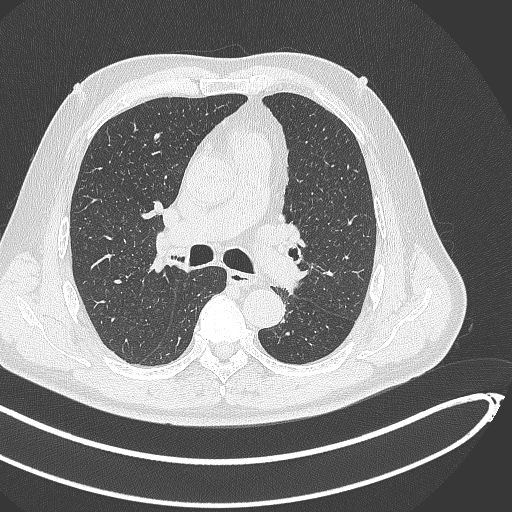
Chest CT, one axial slice. Reconstruction kernel B70f. 120 kVp. Lung window (W 1500 / L -600 HU). 512 × 512 image matrix. Patient: male, 64 years. From the clinical record (not read from this slice): clinical TNM (as recorded): T1c N0 M0.
Outlined on this slice (bounding box drawn by a radiologist):
- lung tumour (recorded histology: squamous cell carcinoma): bounding box <274,270,311,296> (left, top, right, bottom; pixels)